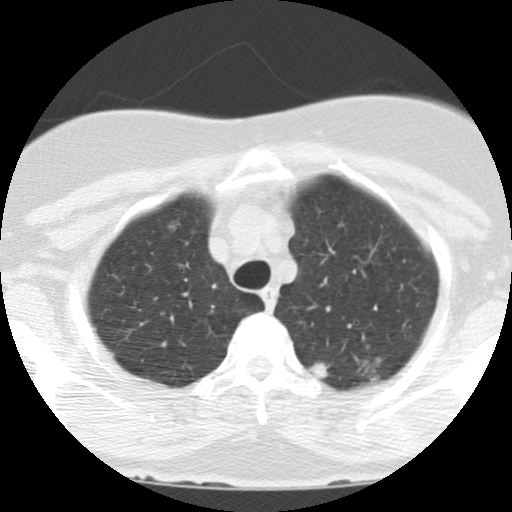
Low-dose screening chest CT, one axial slice. Slice 105 of 123 in the series (ordered by position). Reconstruction kernel STANDARD. 120 kVp. Lung window (W 1500 / L -600 HU). 2.5 mm slice thickness. 512 × 512 image matrix, field of view 290 × 290 mm.
Outlined on this slice (manually delineated by an expert):
- lesion 1 (tumor, upper lobe of left lung): bounding box (x1, y1, x2, y2) in pixels: (308, 363, 327, 379)